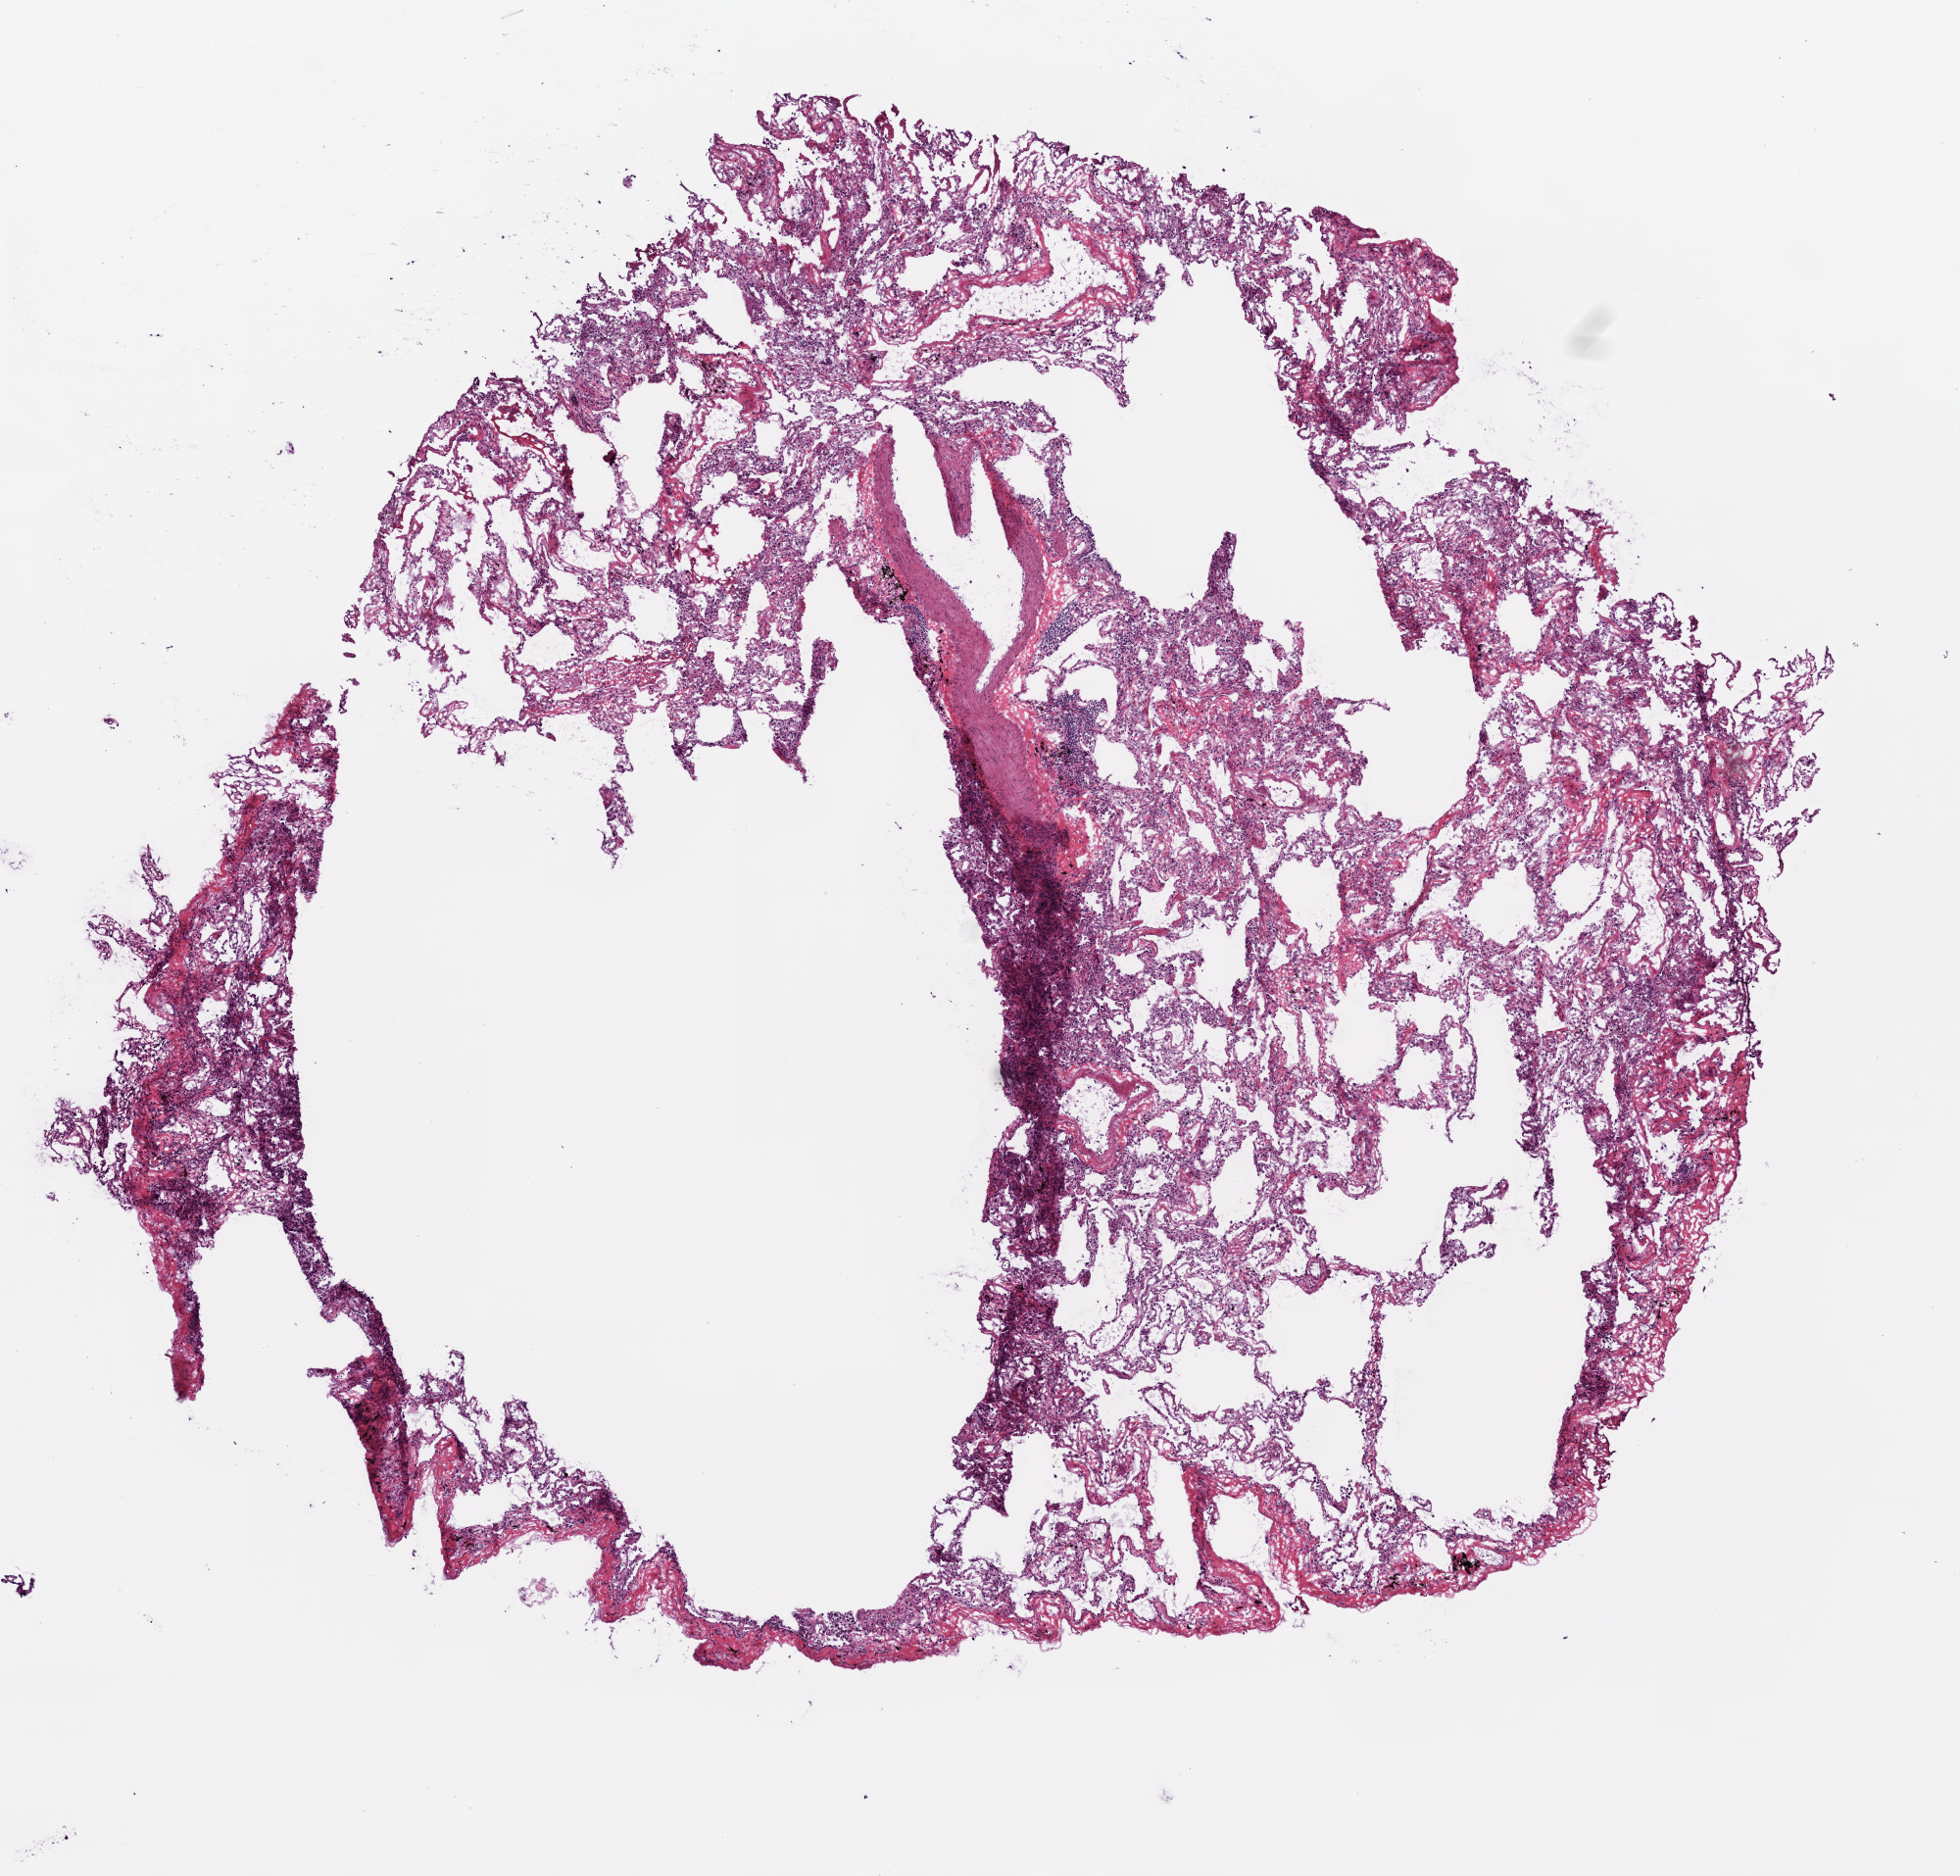
H&E whole-slide image — low-resolution overview of the scanned area, about 8.0 x 7.7 mm, frozen section, lung, solid tissue normal (non-tumour tissue) sample. Patient: female, age at initial diagnosis 73 years.
• this section: solid tissue normal (non-tumour) sample from the same patient
• patient diagnosis: Squamous cell carcinoma, NOS (upper lobe, lung)